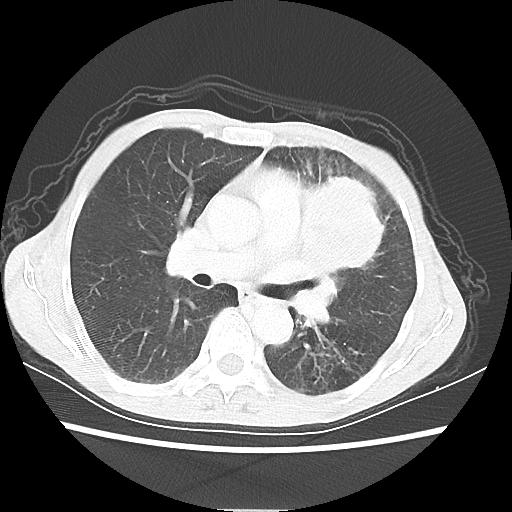
Chest CT, one axial slice. Position 34 of 56 along the scan axis. Reconstruction kernel LUNG. Lung window (W 1500 / L -600 HU). 5 mm slice thickness. 512 × 512 image matrix. Patient: female, 60 years. From the clinical record (not read from this slice): clinical TNM (as recorded): T4 N1 M0.
Structures marked on this image (bounding box drawn by a radiologist):
- lung tumour (recorded histology: adenocarcinoma): box from (x=299, y=175) to (x=398, y=278) px